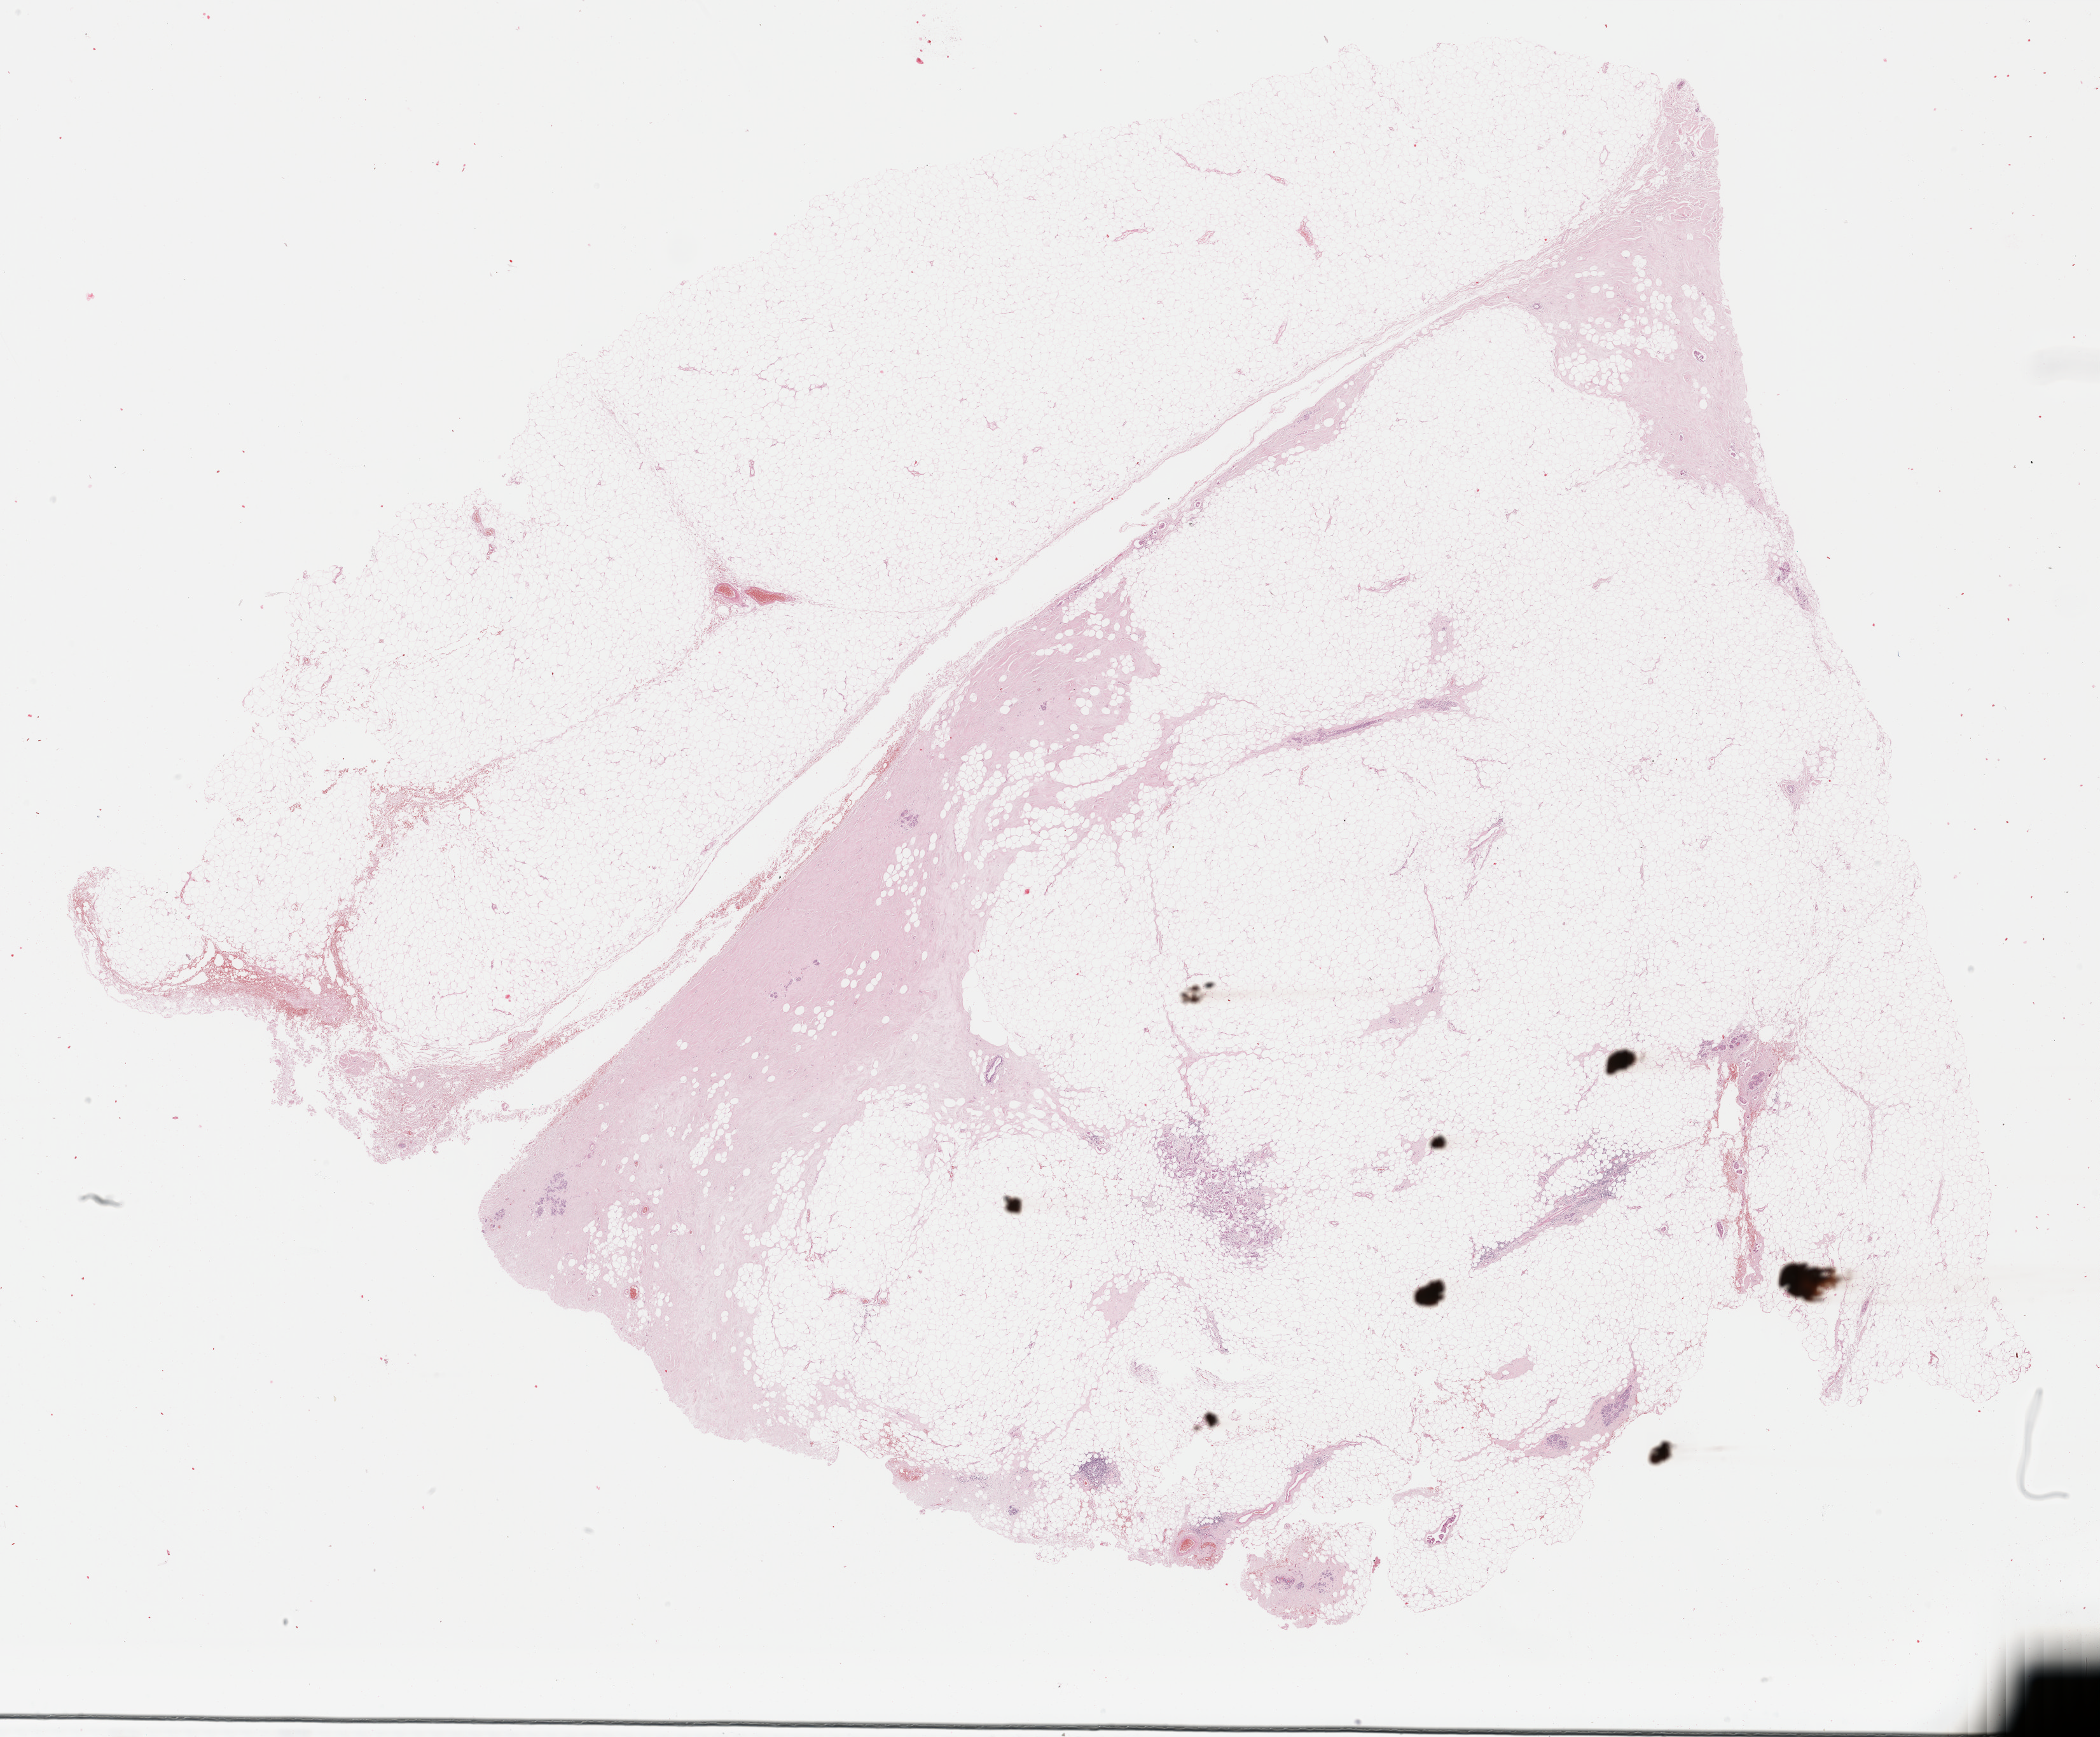
Whole-slide histology image, H&E-stained — whole scanned area (about 26.2 x 21.7 mm, slide scanned at 40x) shown as a low-resolution overview. Formalin-fixed paraffin-embedded (FFPE) diagnostic section. Primary tumour sample from the breast. Patient: female, age at initial diagnosis 59 years.
Histologic diagnosis: Infiltrating duct carcinoma, NOS.